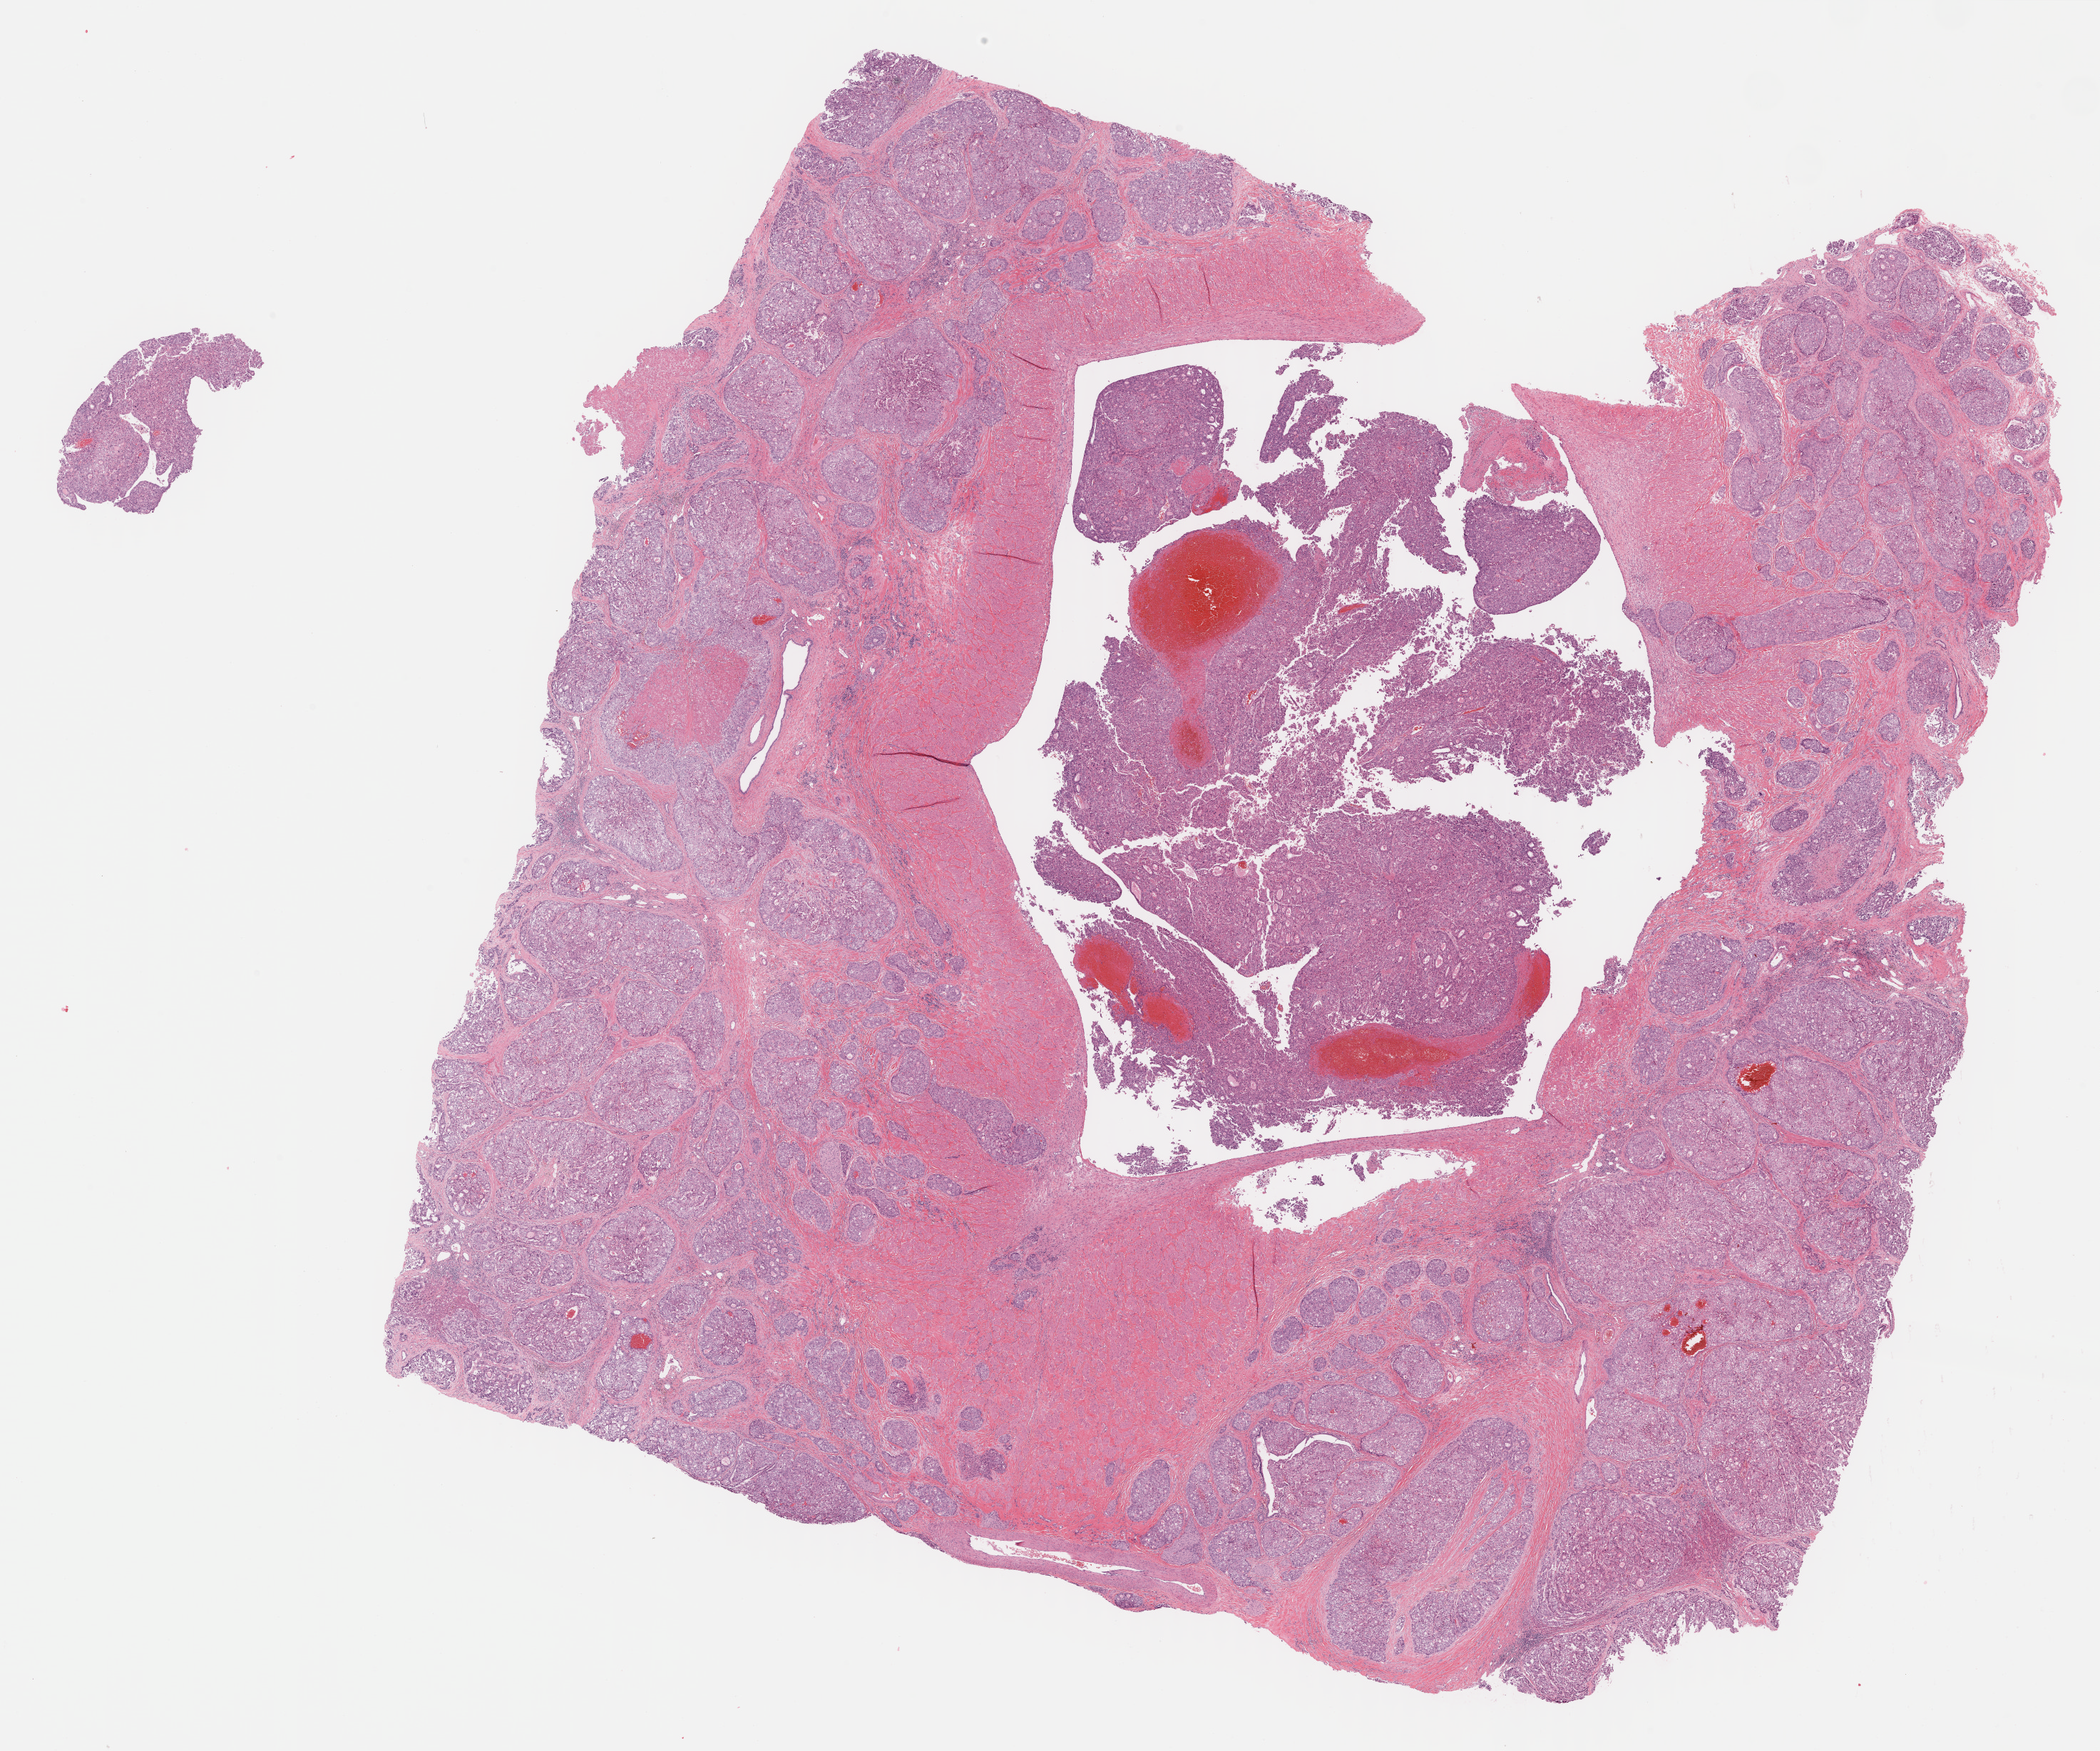
Hematoxylin and eosin (H&E) stained whole-slide image — low-resolution overview of the scanned area, about 23.8 x 19.9 mm (slide scanned at 40x); formalin-fixed paraffin-embedded (FFPE) diagnostic section; bile duct, primary tumour sample. Patient: male, age at initial diagnosis 81 years. Histologic grade: G4 (undifferentiated).
- pathologic diagnosis: Cholangiocarcinoma
- AJCC pathologic stage: II (7th edition)
- TNM: T2 N0 M0